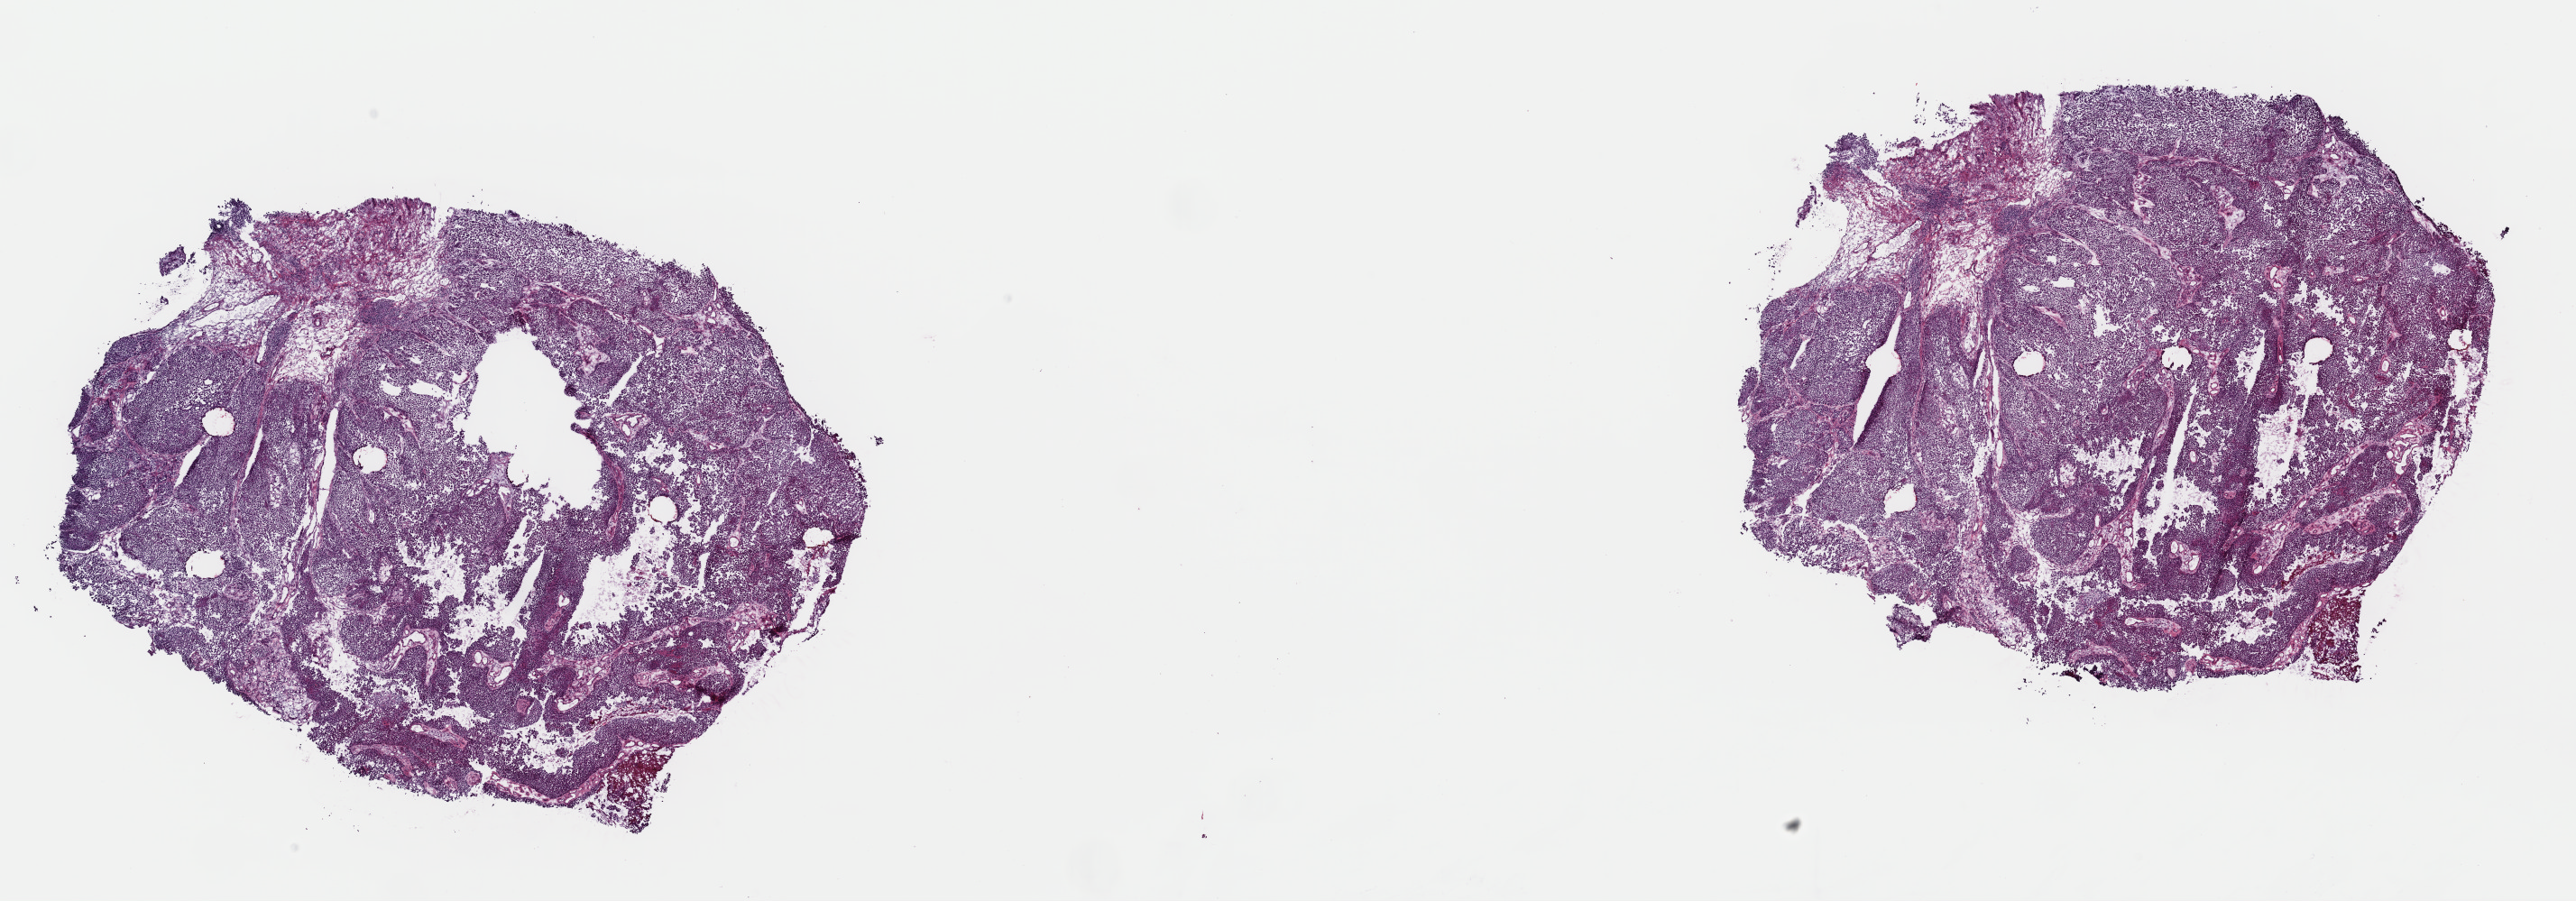
Hematoxylin and eosin (H&E) stained whole-slide image, low-resolution overview of the scanned area, about 22.6 x 7.9 mm (acquisition: 40x scan). Frozen section. Bladder, primary tumour sample. Patient: male, age at initial diagnosis 70 years. Histologic grade: high grade. Slide review estimates, as recorded: tumour cells 89%, tumour nuclei 97%, normal cells 0%, stromal cells 10%, necrosis 1%. Infiltration values recorded for this section: lymphocyte infiltration 3%, monocyte infiltration 0%, neutrophil infiltration 0%.
AJCC pathologic stage: II (7th edition). Diagnosis: Transitional cell carcinoma (dome of bladder). TNM: T2b N0 M0. Lymph nodes positive (case pathology): 0 of 2 examined.